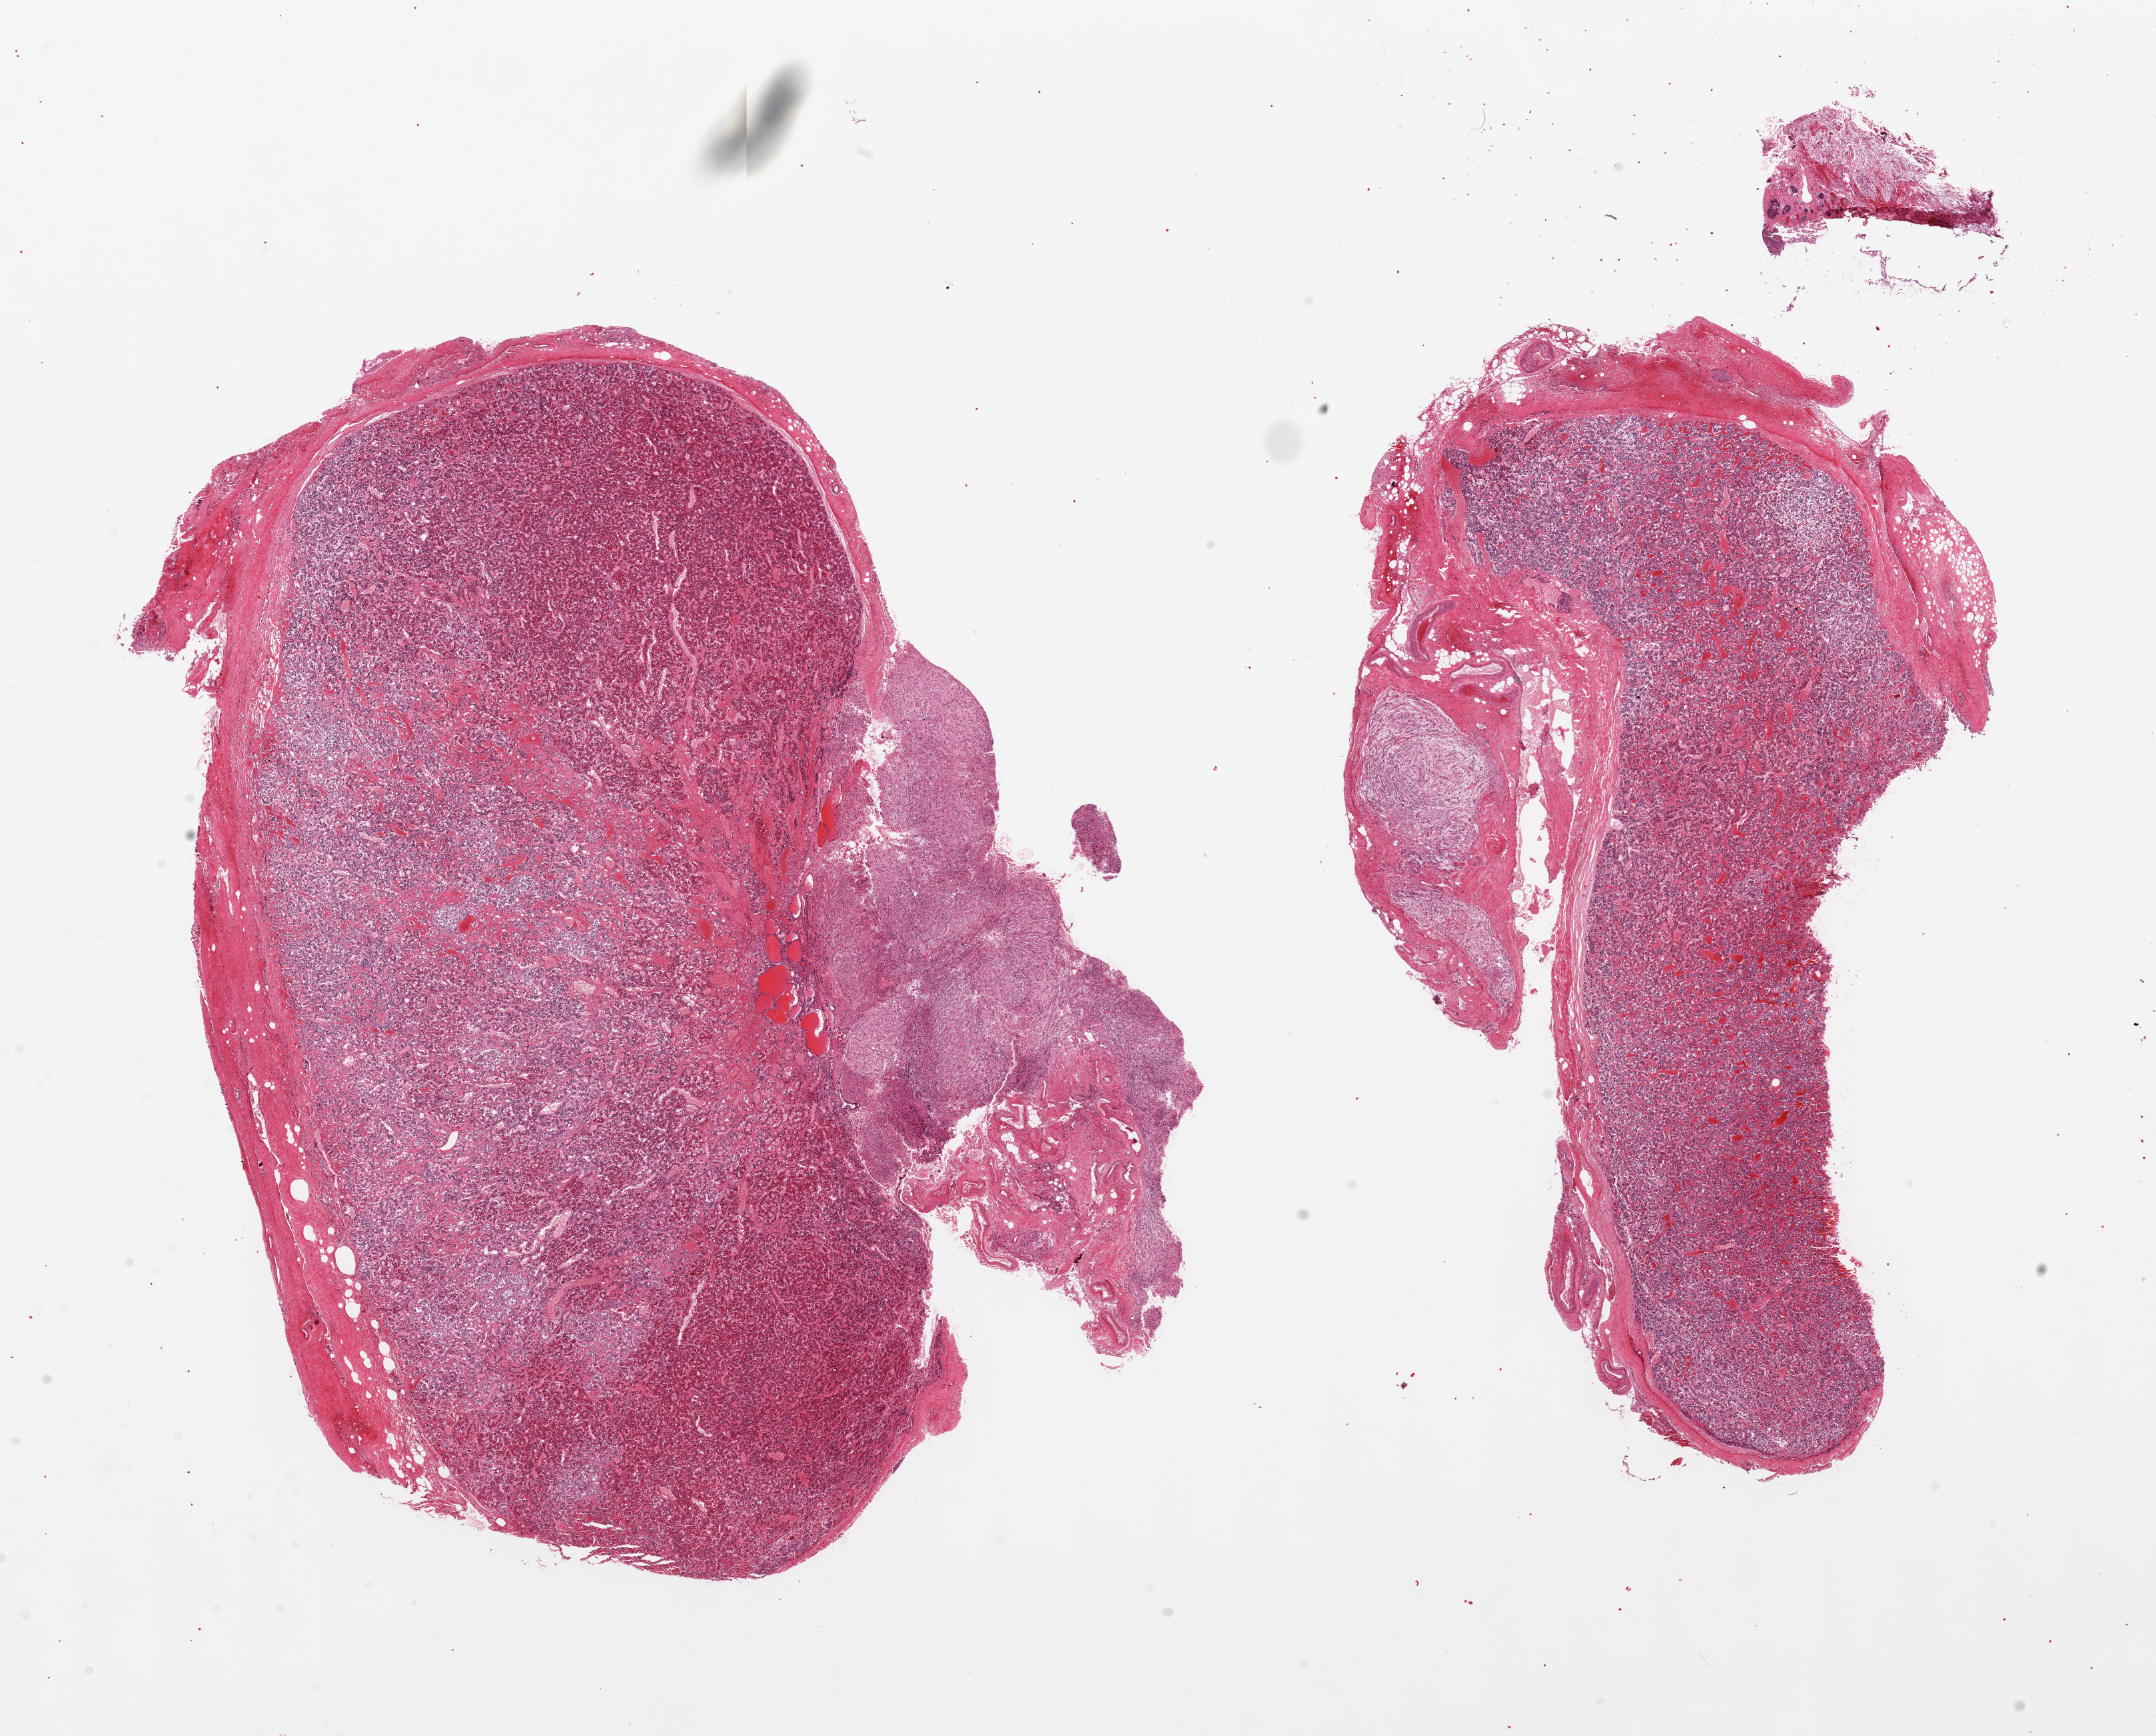
Digitized H&E-stained section — low-resolution overview of the scanned area, about 25.6 x 20.6 mm, PAXgene-fixed, paraffin-embedded tissue, target tissue: pituitary, tissue donor sample.
Pathologist's review note for this sample: 2 pieces, 90% adenohypophysis/ 10% neurohypophysis.